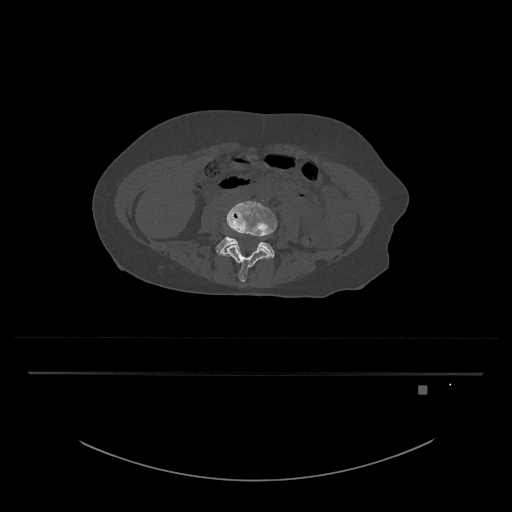
CT including the spine, one axial slice. Slice 340 of 797 in the series (ordered by position). 120 kVp. Bone window (W 1800 / L 400 HU). 0.5 mm slice thickness. 512 × 512 image matrix, field of view 500 × 500 mm. Patient: female, 57 years. From the clinical record (not read from this slice): primary cancer: cervical.
Structures marked on this image (semi-automatic segmentation, software-assisted and operator-edited):
- L4 vertebra: bounding box <220,201,277,282> (left, top, right, bottom; pixels)